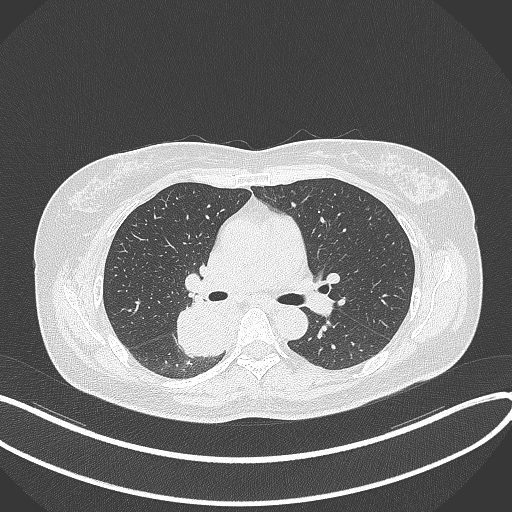
Chest CT, one axial slice; slice 216 of 331 in the series (ordered by position); lung window (W 1500 / L -600 HU); 512 × 512 image matrix. Patient: female, 54 years. Case-level facts recorded for this patient, not image findings: clinical TNM (as recorded): T4 N0 M0.
Annotated regions visible in this slice (rectangle marked by the reading radiologist):
- lung tumour (recorded histology: adenocarcinoma): bounding box (x1, y1, x2, y2) in pixels: (172, 294, 230, 363)